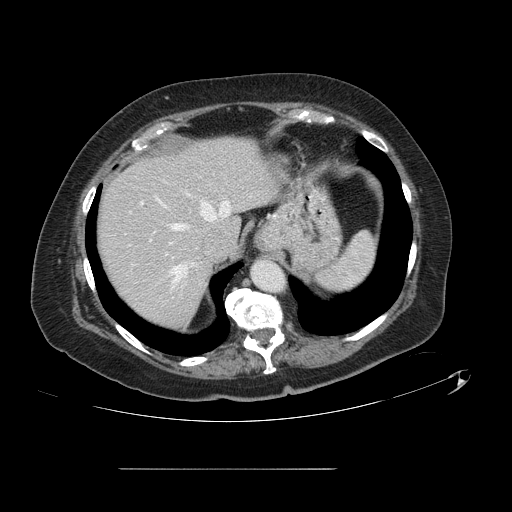
Contrast-enhanced abdominal CT, one axial slice. Slice 109 of 148 in the series (ordered by position). Intravenous contrast given. Soft-tissue window (W 400 / L 40 HU). 512 × 512 image matrix, field of view 439 × 439 mm. Female patient, age 75 years. From the clinical record (not read from this slice): diagnosis: colorectal cancer liver metastases, imaged before liver resection; multiple liver metastases: no; largest metastasis: 2.4 cm; disease in both lobes: no.
Annotated regions visible in this slice (outlined manually by an expert reader):
- hepatic veins: box from (x=156, y=198) to (x=232, y=282) px
- liver: (x=96, y=137)–(x=273, y=328)
- planned liver remnant (the part of the liver to remain after resection): (x=96, y=137)–(x=273, y=328)
- portal vein (with intrahepatic branches): (x=141, y=202)–(x=143, y=204)